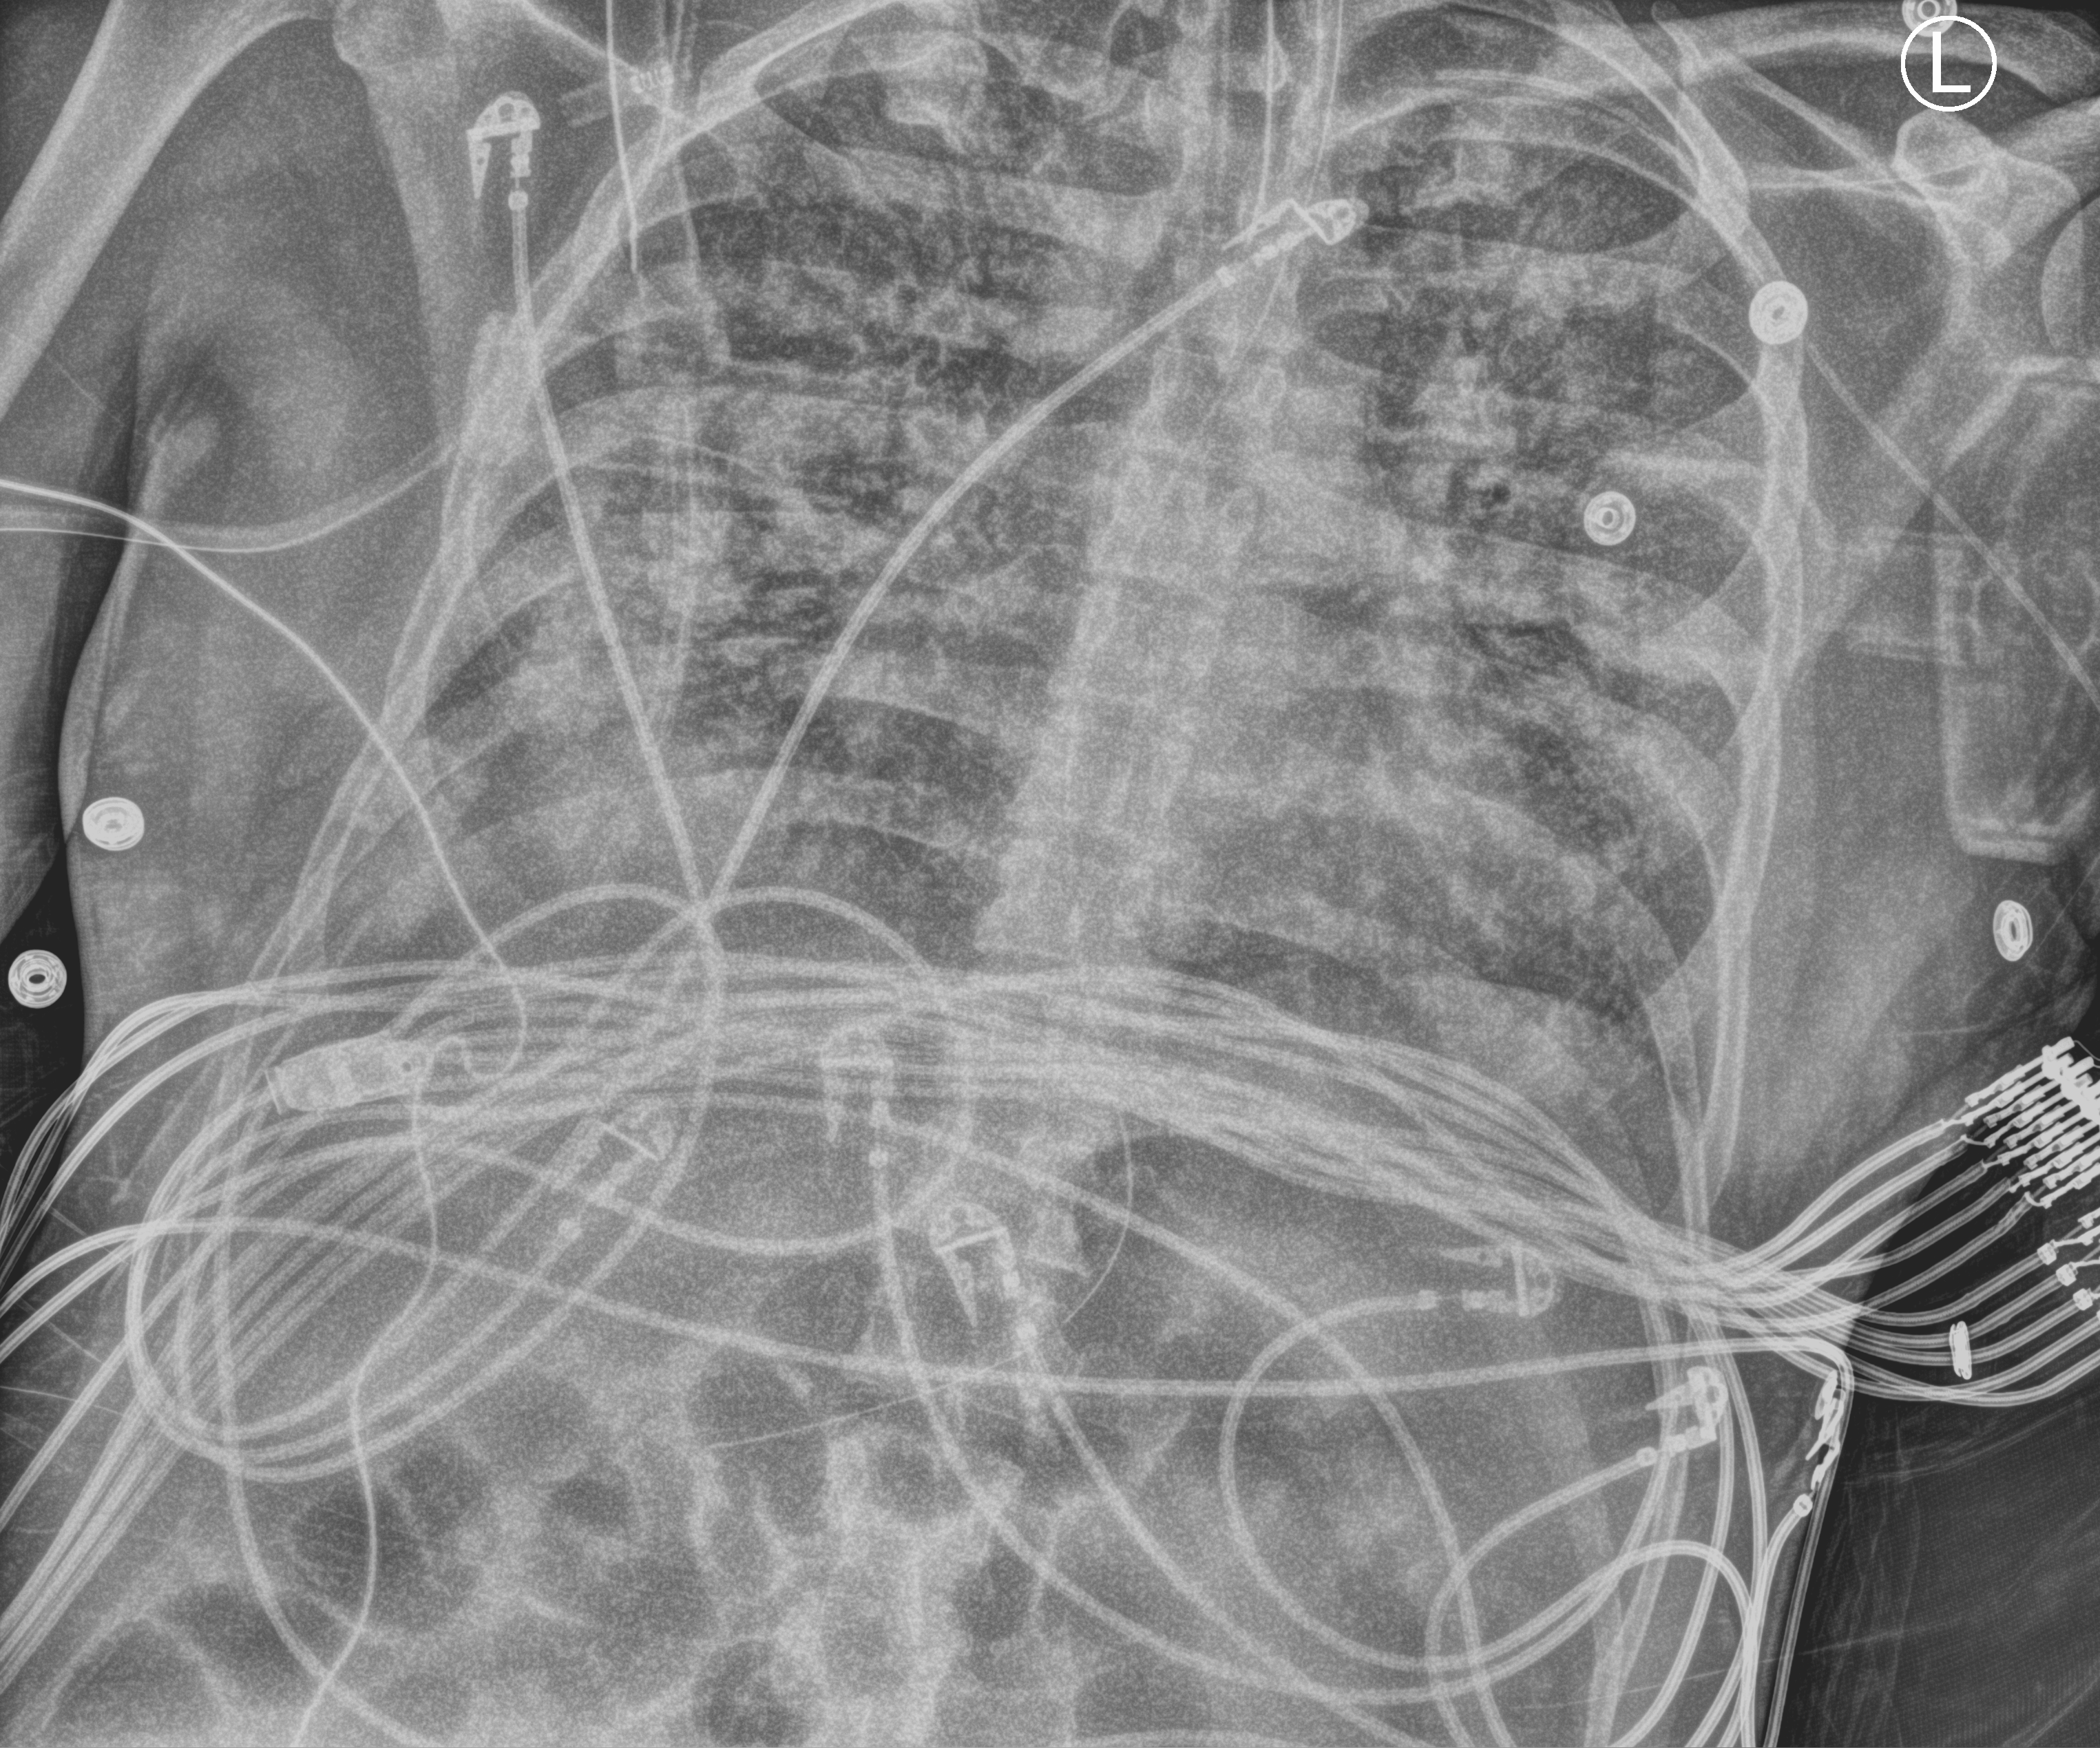
Bedside chest radiograph (computed radiography); anteroposterior (AP) projection. Patient hospitalised with COVID-19; male, aged 18–59 years.
From the hospital-stay record, not from the radiograph (when in the stay this image was taken is not recorded): chronic kidney disease (admission record): no; admitted to intensive care during this hospital stay: yes.